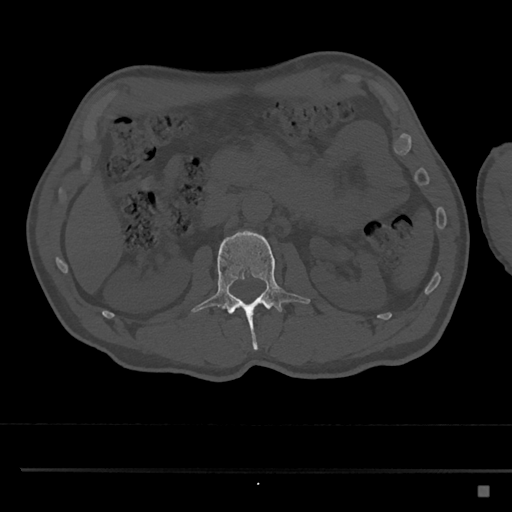
CT including the spine, one axial slice; position 765 of 797 along the scan axis; reconstruction kernel Br40s/3; 120 kVp; bone window (W 1800 / L 400 HU); 0.5 mm slice thickness; 512 × 512 image matrix. Male patient, age 59 years. From the clinical record (not read from this slice): primary cancer: prostate.
Structures marked on this image (semi-automatically segmented with operator editing):
- L2 vertebra: bounding box <192,230,310,351> (left, top, right, bottom; pixels)